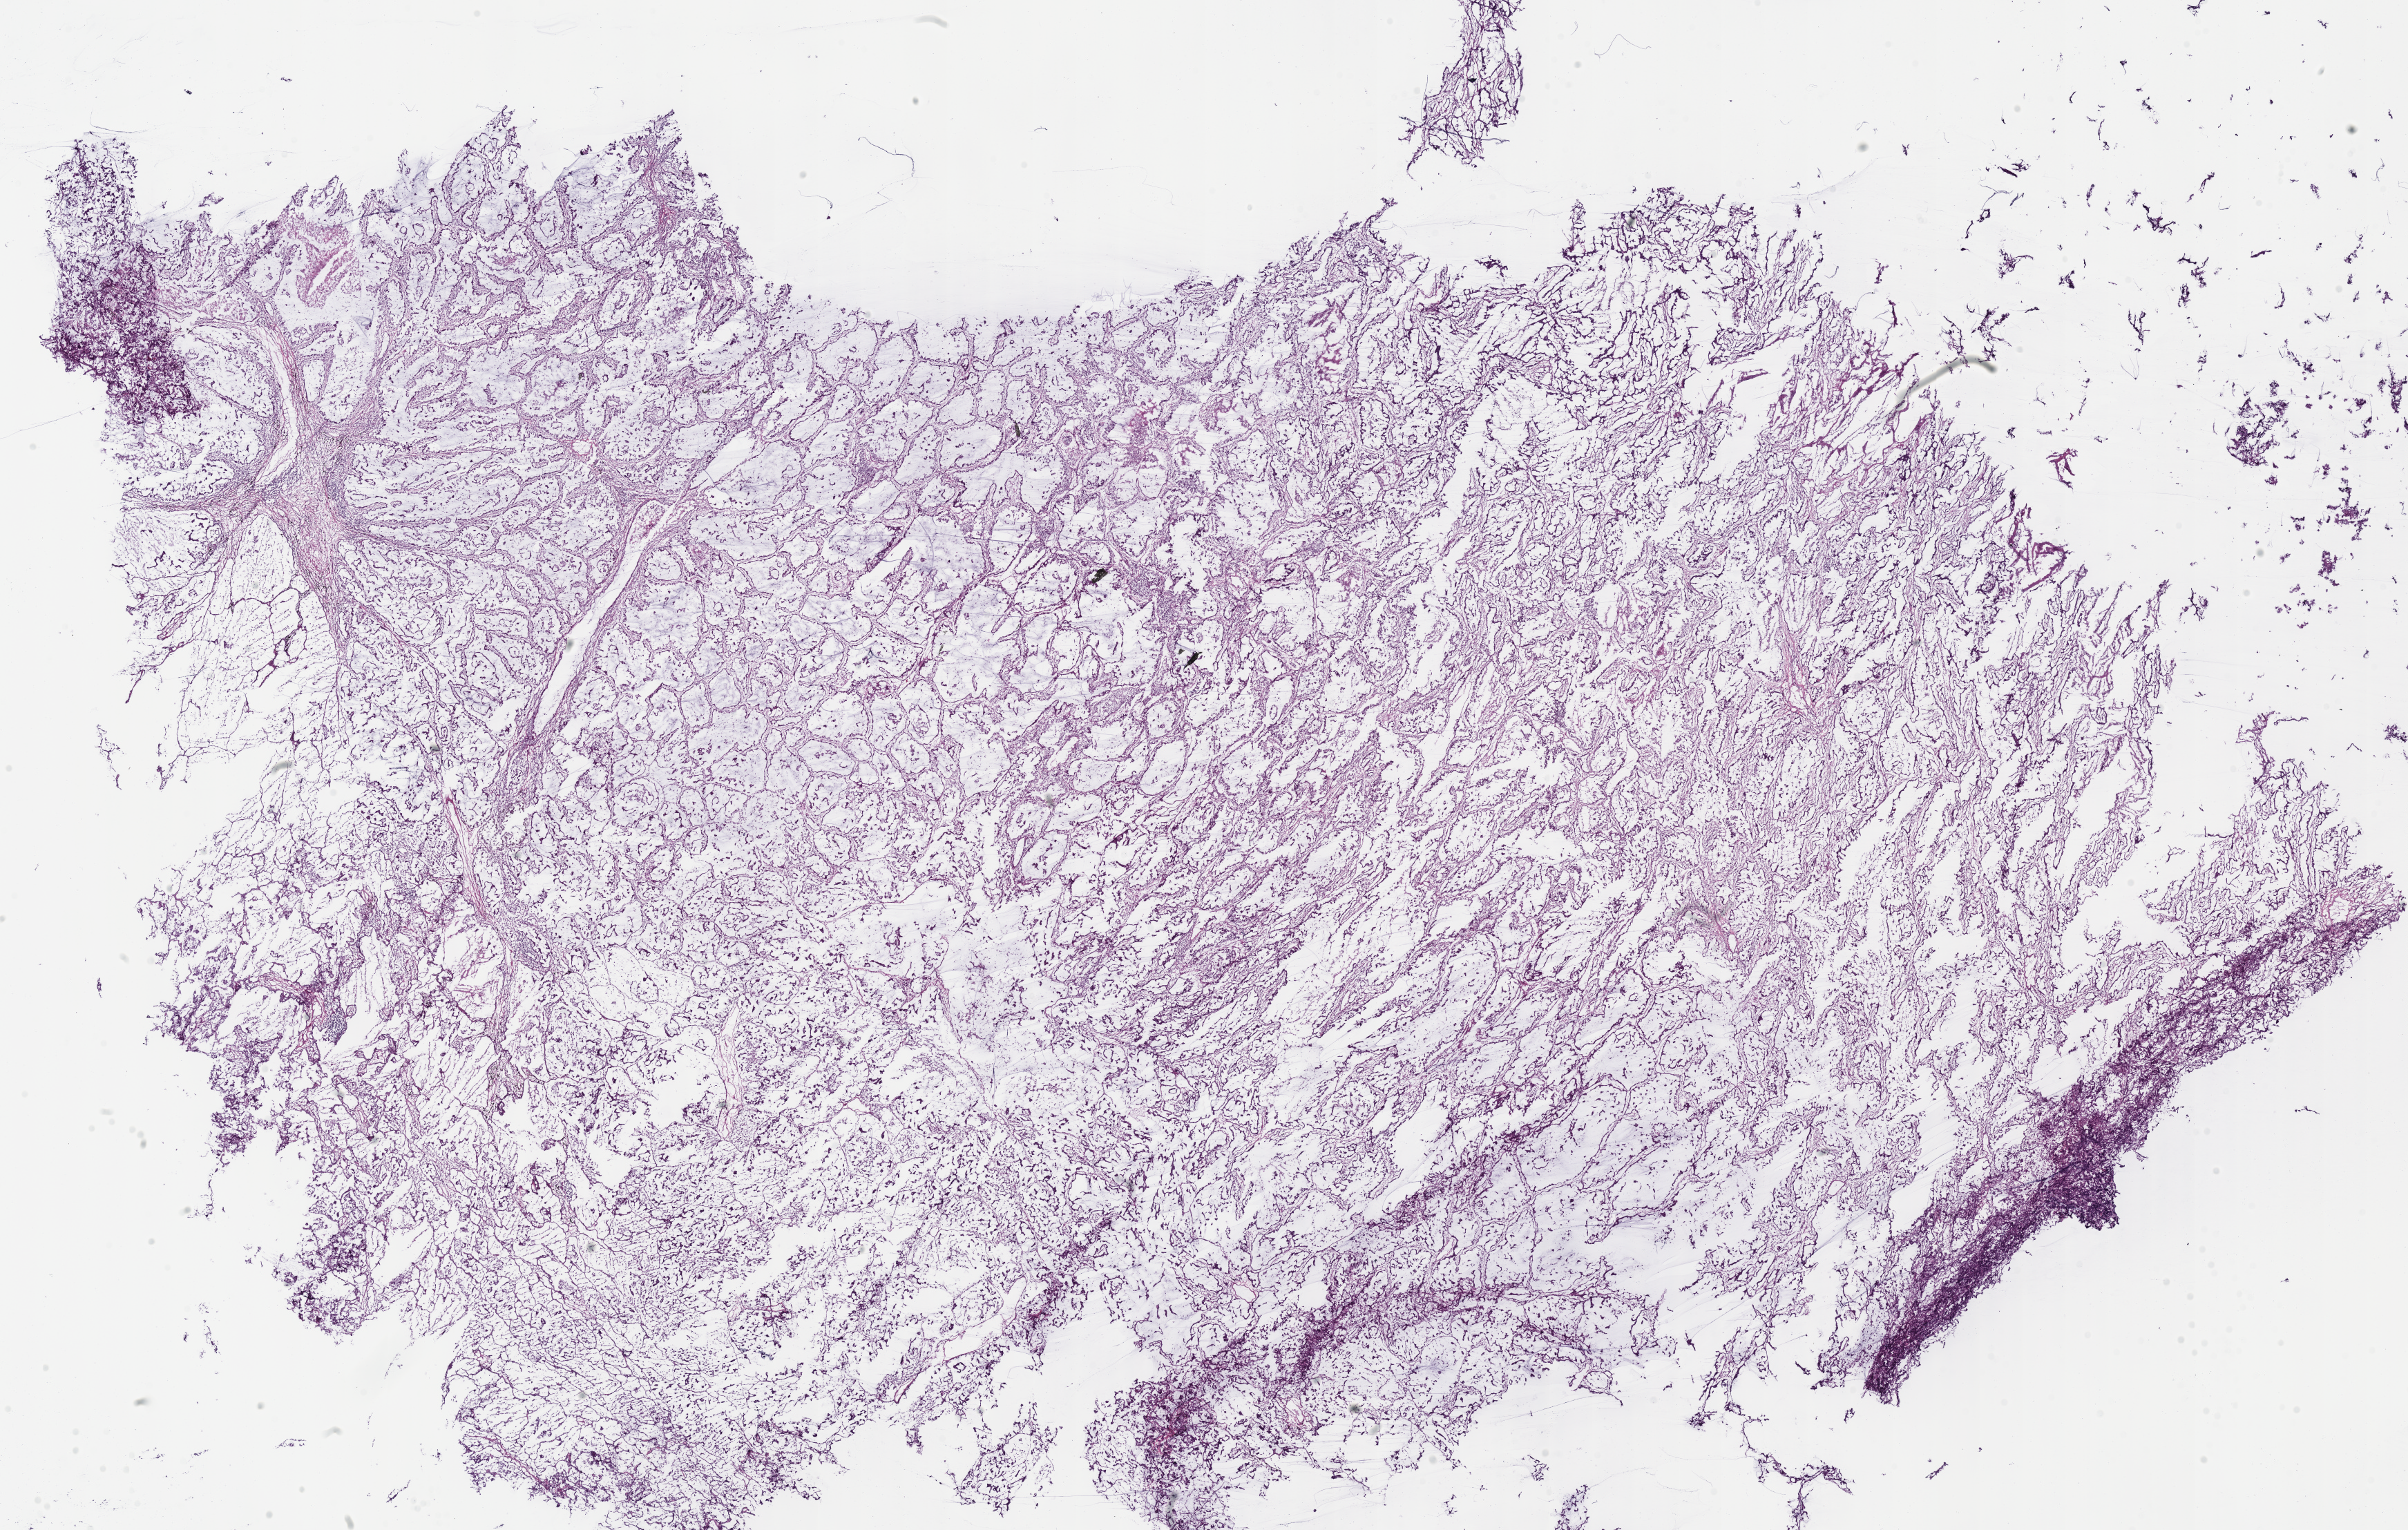
Whole-slide histology image, H&E — a low-resolution overview of the entire scanned area, about 27.4 x 17.4 mm (acquisition: 40x scan); frozen section; lung, primary tumour sample. Patient: male, age at initial diagnosis 52 years. Slide review estimates, as recorded: tumour cells 85%, tumour nuclei 75%, normal cells 0%, stromal cells 15%, necrosis 0%.
- histologic diagnosis: Adenocarcinoma, NOS
- TNM: T3 N2 M0
- AJCC pathologic stage: IIIA (7th edition)
- laterality: left